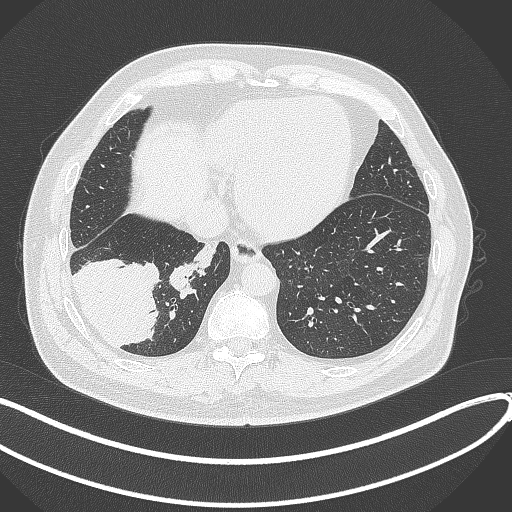
Chest CT, one axial slice; slice 93 of 360 in the series (ordered by position); reconstruction kernel B70f; lung window (W 1500 / L -600 HU); 1 mm slice thickness; 512 × 512 image matrix. Patient: male, 59 years.
Outlined on this slice (bounding box drawn by a radiologist):
- lung tumour (recorded histology: adenocarcinoma): bounding box (x1, y1, x2, y2) in pixels: (63, 250, 163, 350)